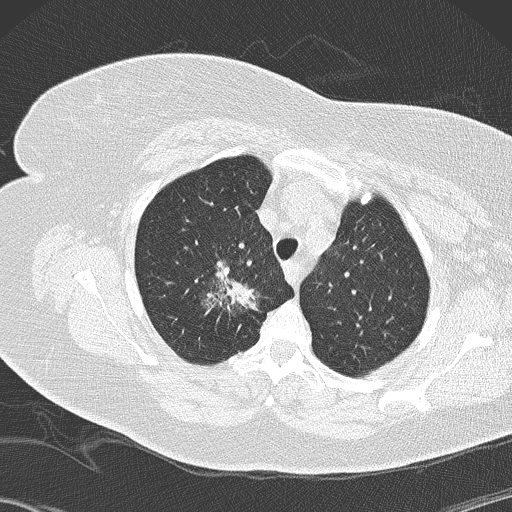
Chest CT (low-dose screening protocol), one axial image; second annual screen; lung window (W 1500 / L -600 HU); lung (sharp) reconstruction kernel (B50f); slice 31 of 146 in the series. Female, age 72 years at enrolment.
Expert reader's lesion annotation, bounding box <179,241,262,327> (left, top, right, bottom; pixels). The screening reader recorded 4 non-calcified nodules or masses ≥4 mm on this exam; which of them this box marks is not recorded. Official screen result: positive, other. Participant outcome: lung cancer diagnosed 52 days after this screen — bronchiolo-alveolar adenocarcinoma, NOS, right upper lobe, stage IIIB (AJCC 6th edition), 45 mm at pathology.